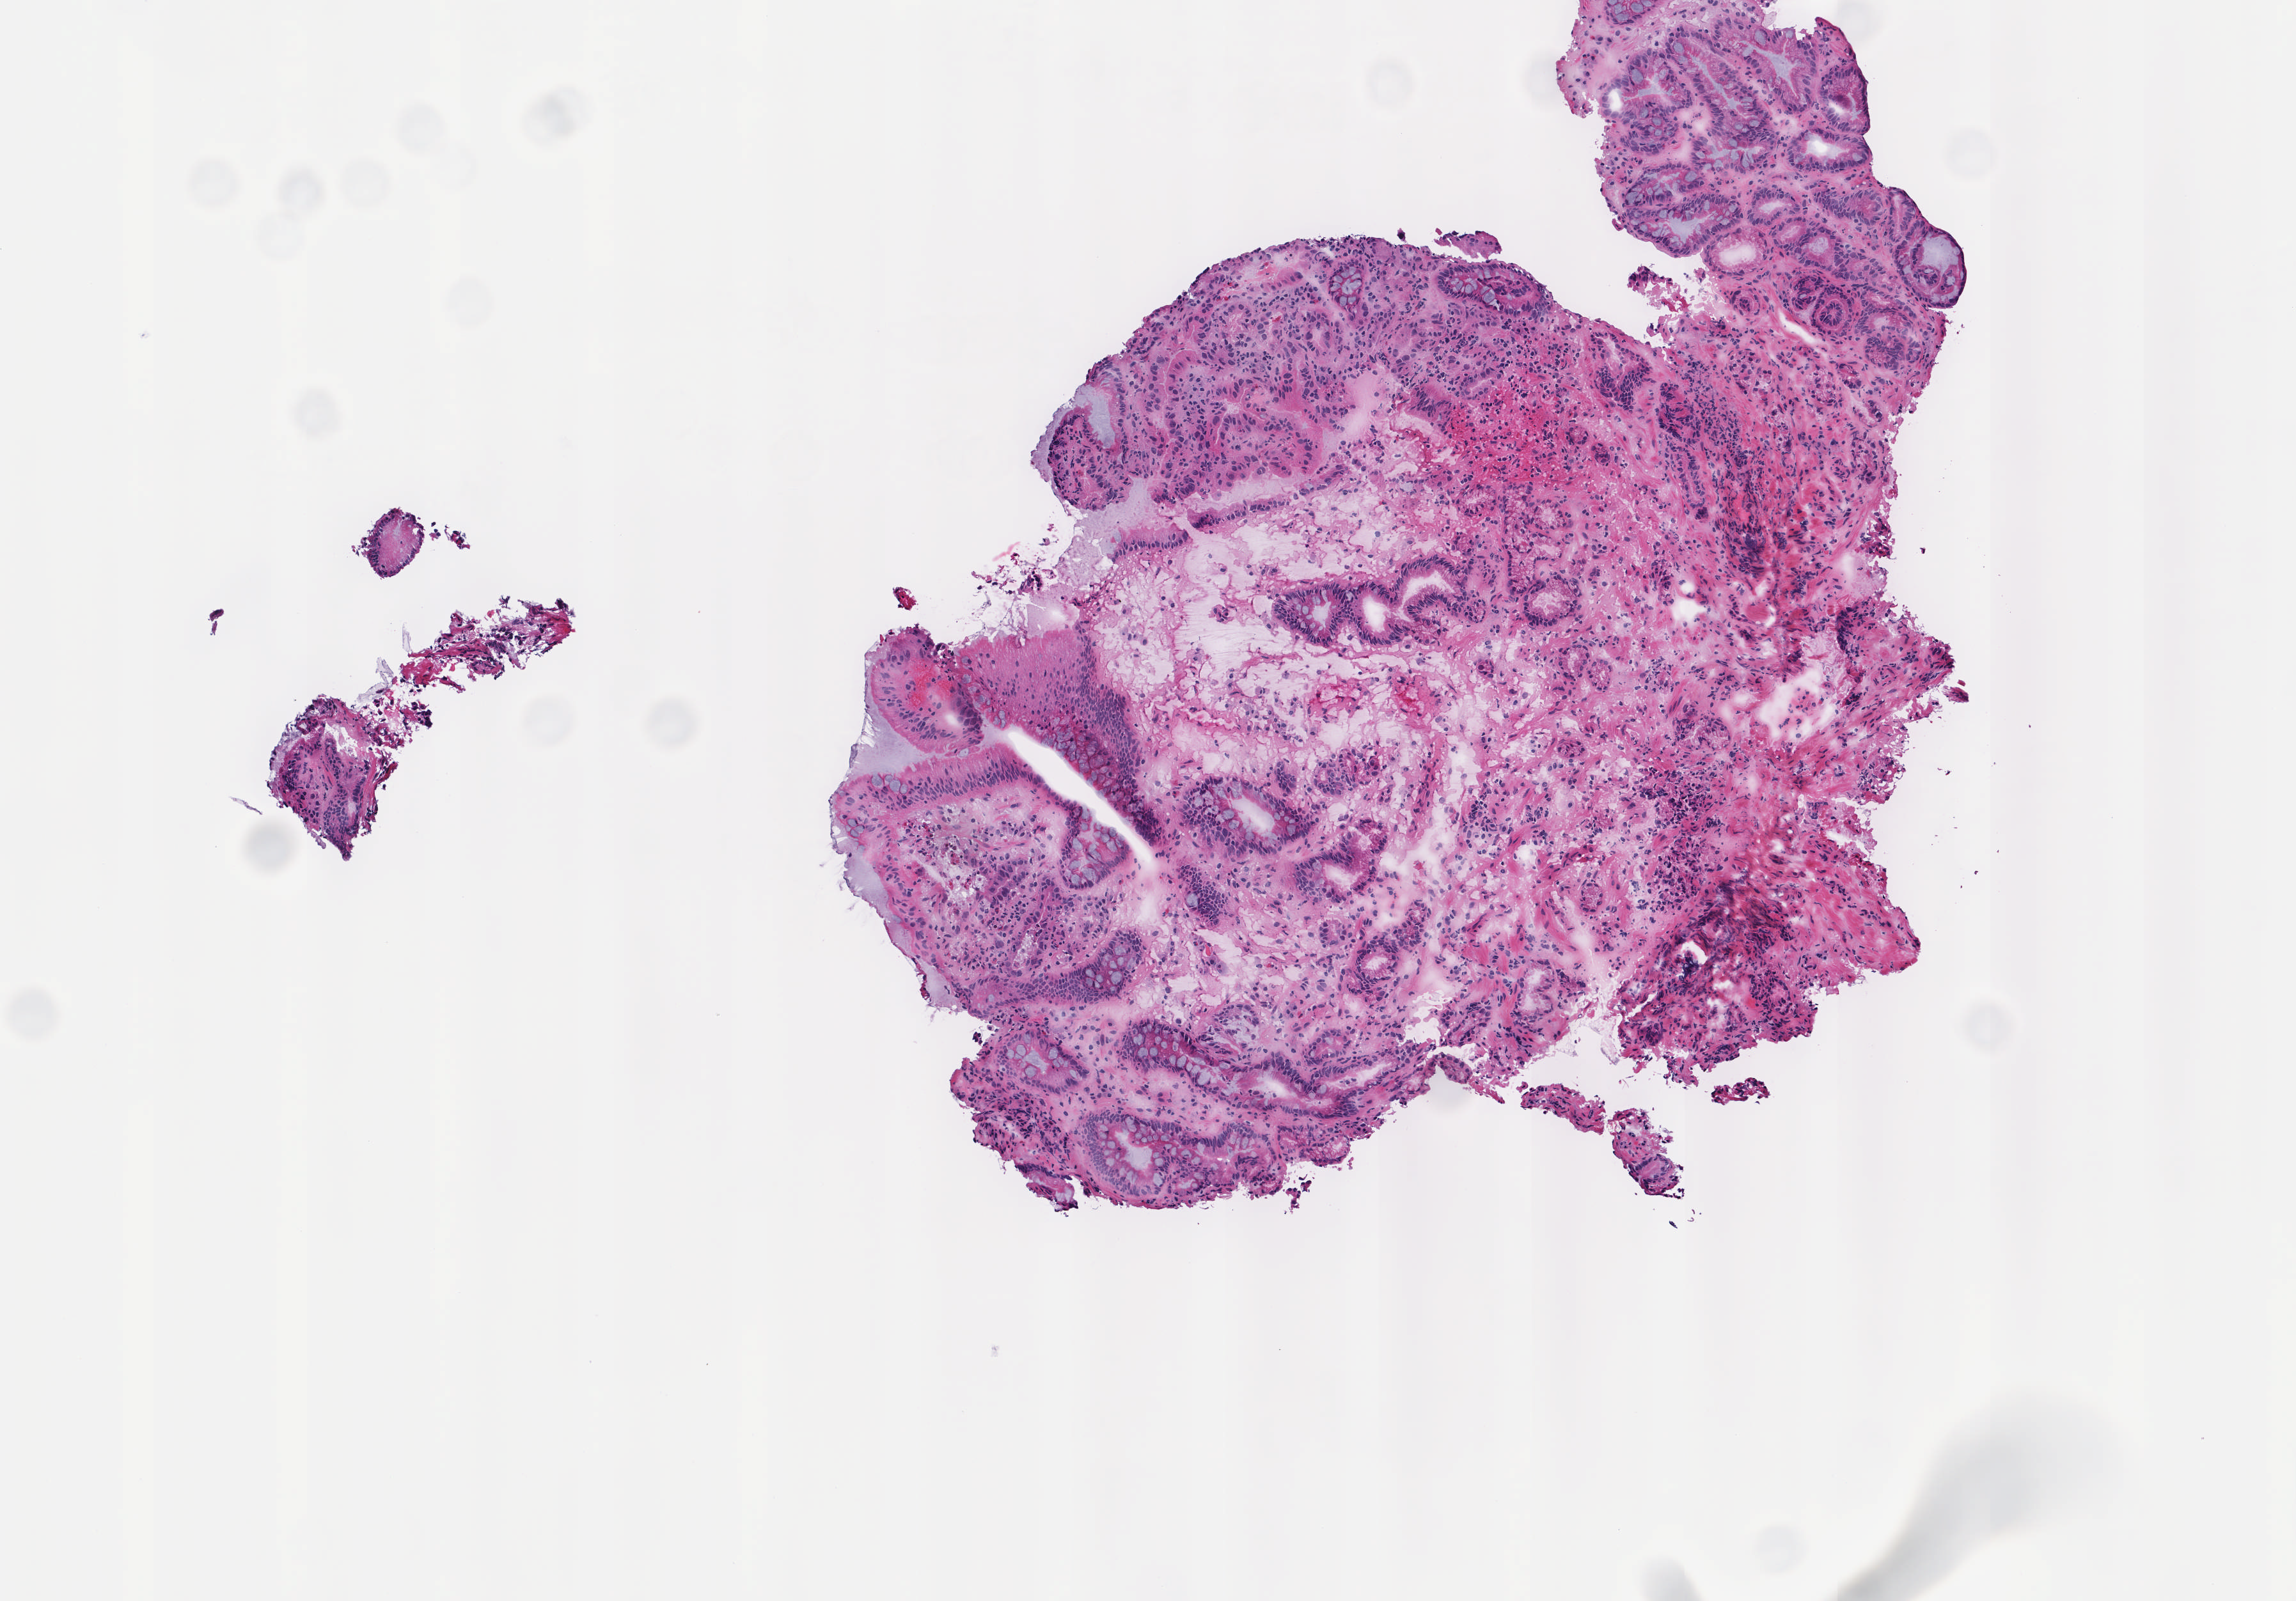
Whole-slide histology image, H&E — shown as a low-resolution overview of the whole scanned area (about 3.6 x 2.5 mm, slide scanned at 40x). Frozen section from the top of the tissue portion. Sample: solid tissue normal (non-tumour tissue), esophagus. Male, age 45 years at initial diagnosis. Pathologist review of this section (percent, as recorded): tumour cells 0%, tumour nuclei 0%, normal cells 100%, stromal cells 0%, necrosis 0%. Inflammatory infiltration, as recorded: lymphocyte infiltration 5%, monocyte infiltration 4%, neutrophil infiltration 1%.
This section: solid tissue normal (non-tumour) sample from the same patient. Patient diagnosis: Adenocarcinoma, NOS (middle third of esophagus).